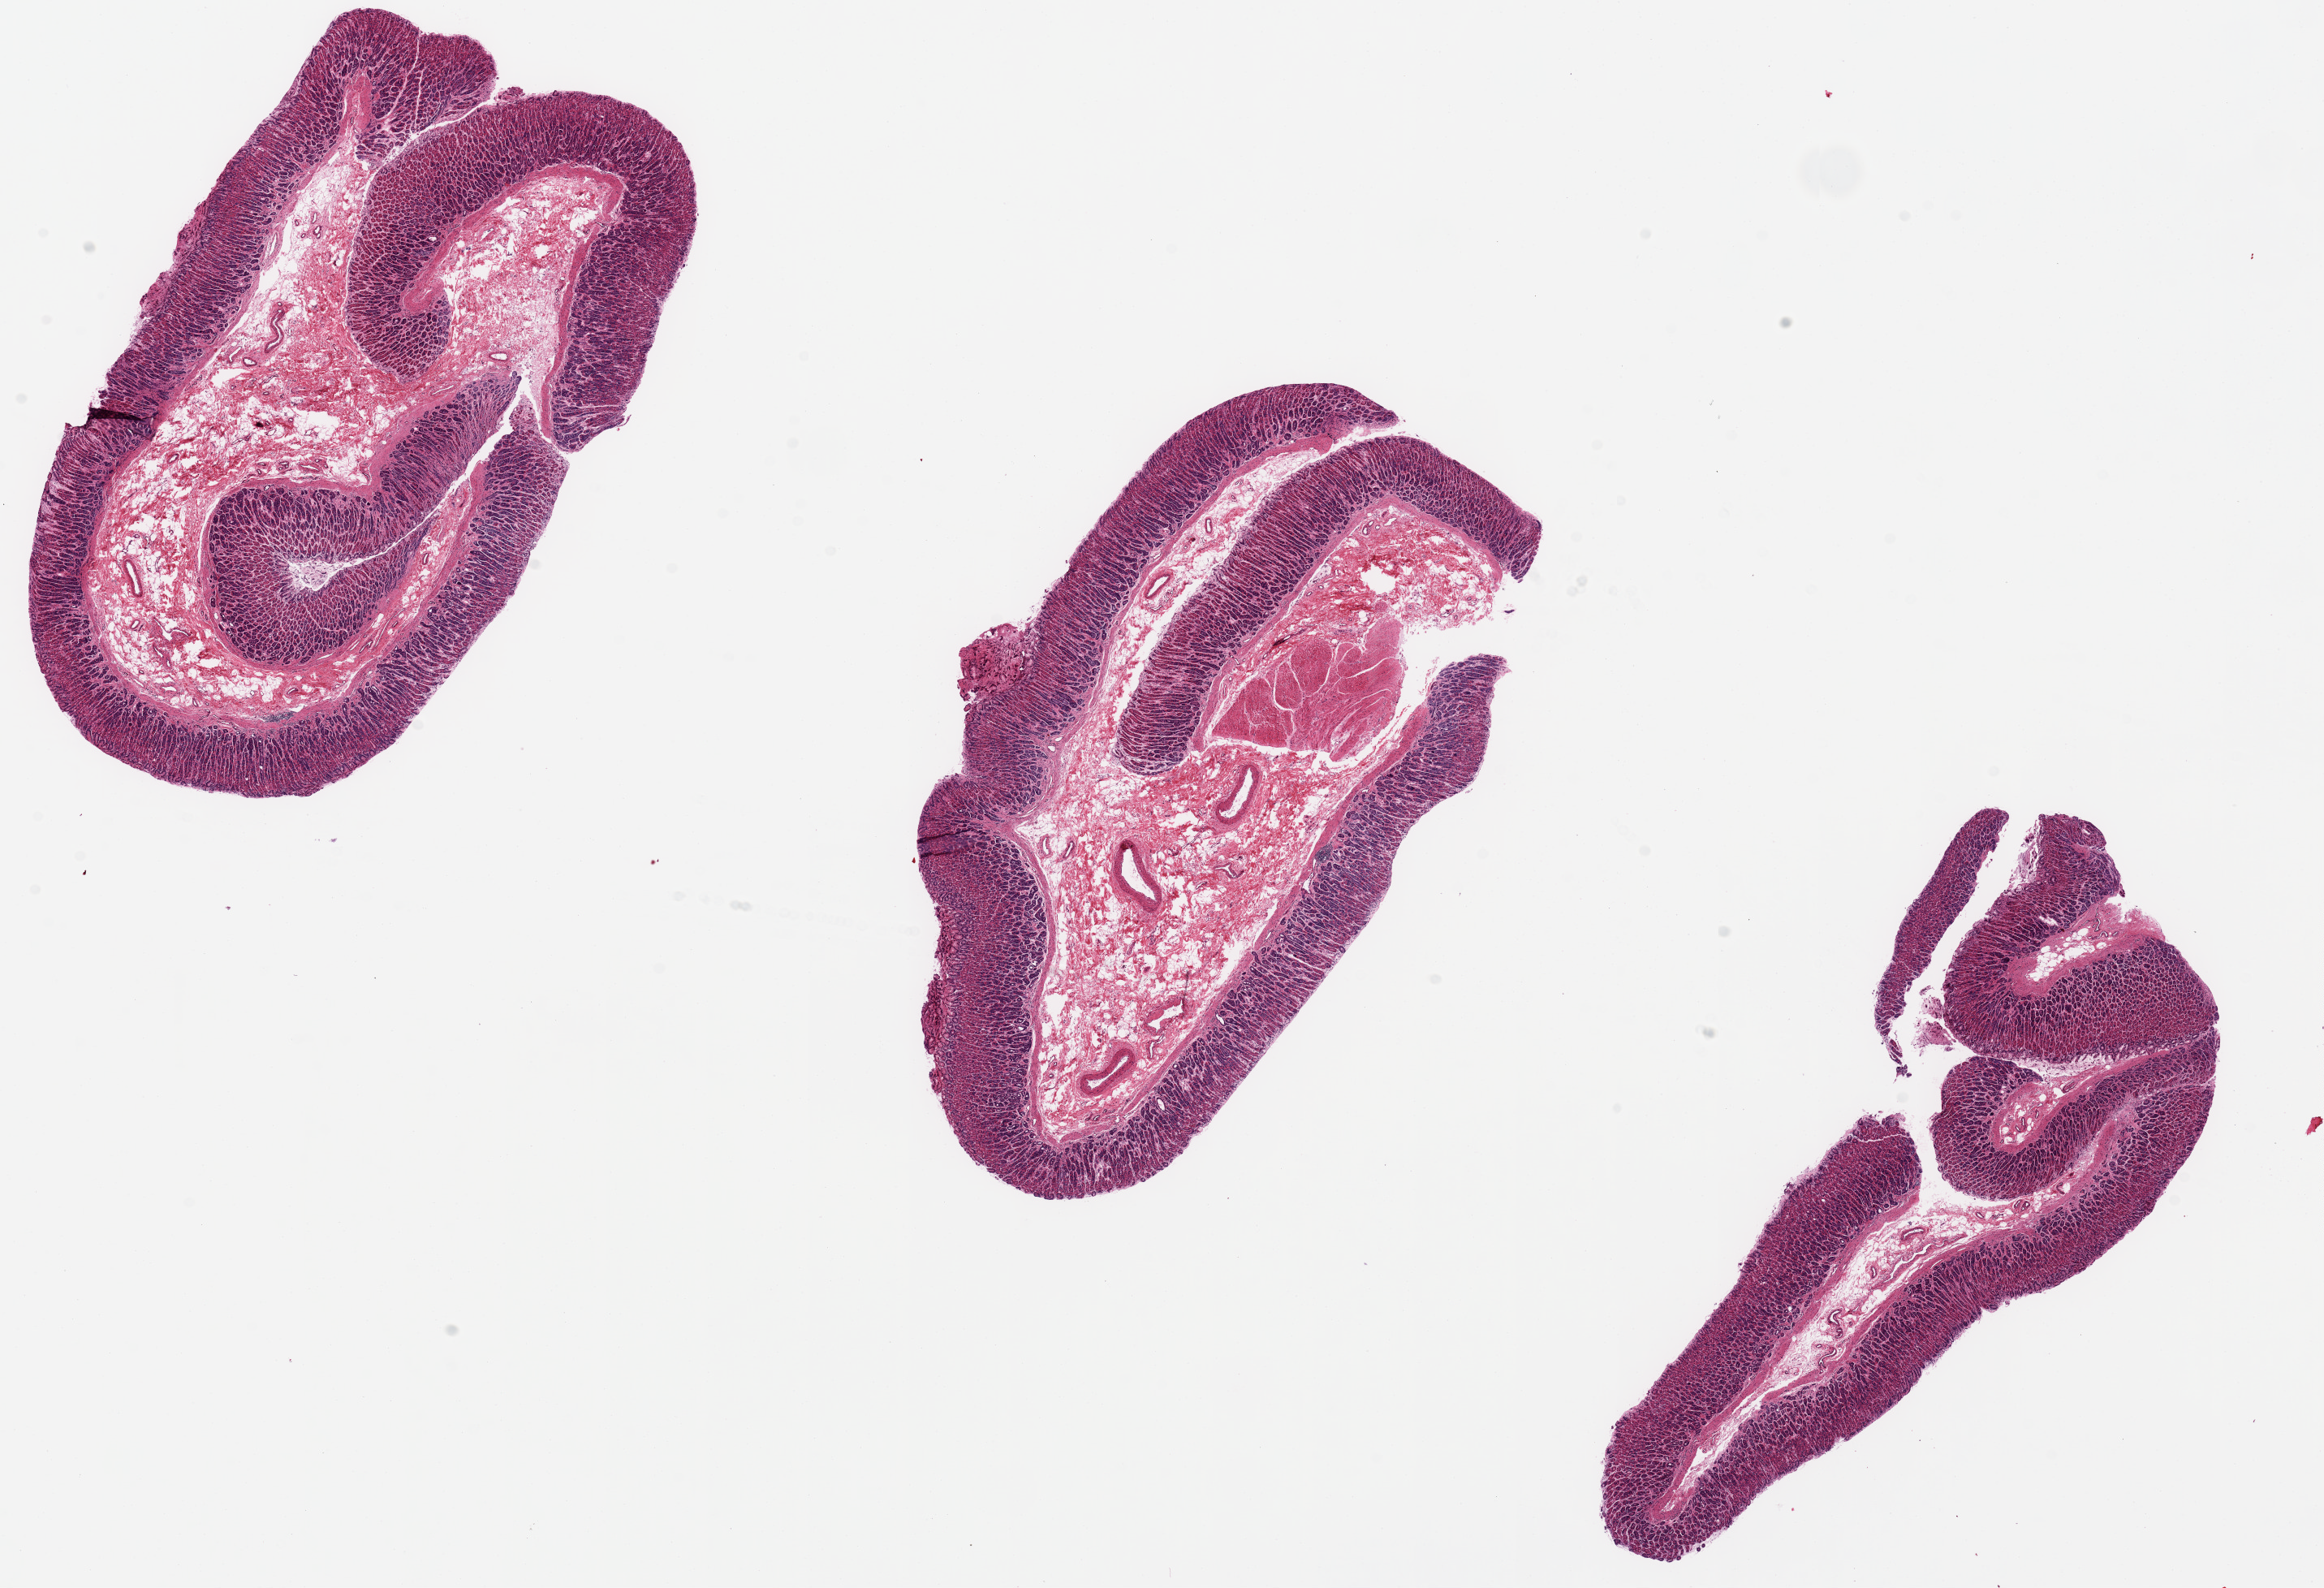
Digitized haematoxylin and eosin-stained section, low-resolution overview of the scanned area, about 22.6 x 15.5 mm (from a 20x scan), PAXgene-fixed, paraffin-embedded tissue, section of stomach (target tissue), tissue donor sample. Donor: male.
Review note (as recorded): Gastric body mucosa with little muscle and much mucosa.